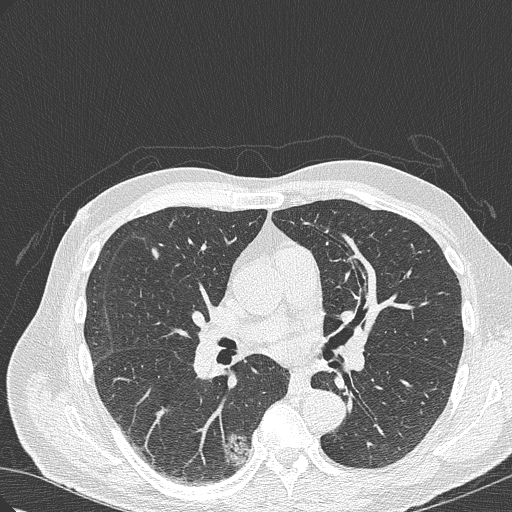
Axial slice from a low-dose chest CT screening exam. First (baseline) screen. Lung window (W 1500 / L -600 HU). Slice 144 of 322 in the series. 512 × 512 image matrix. Male, age 70 years at enrolment. Current smoker at enrolment.
Lesion marked by an expert reader, bounding box (x1, y1, x2, y2) in pixels: (198, 420, 261, 479). The screening reader recorded 4 non-calcified nodules or masses ≥4 mm on this exam (right lower lobe, right lower lobe, right upper lobe, right lower lobe); which of them this box marks is not recorded. Later outcome: lung cancer diagnosed 978 days after this screen (after the third annual screen) — bronchiolo-alveolar adenocarcinoma, NOS, right lower lobe, poorly differentiated (G3), stage IB (AJCC 6th edition), 30 mm at pathology.